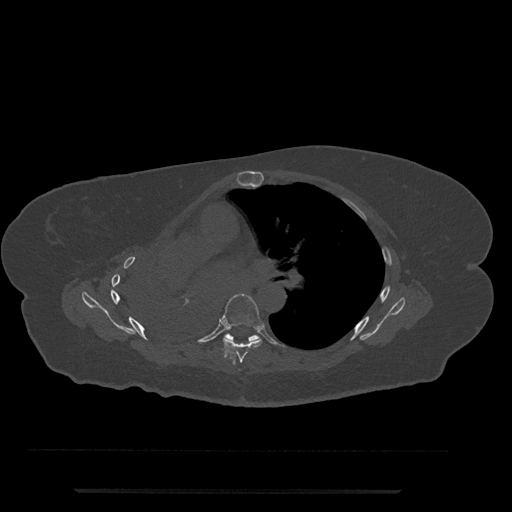
CT including the spine, one axial slice; position 480 of 797 along the scan axis; bone window (W 1800 / L 400 HU); 0.5 mm slice thickness; 512 × 512 image matrix, field of view 440 × 440 mm. Patient: female, 51 years. From the clinical record (not read from this slice): primary cancer: neuro; vertebrae with lytic lesions (as recorded): T8.
Outlined on this slice (semi-automatically segmented with operator editing):
- T6 vertebra: bounding box [x1, y1, x2, y2] px = [220, 294, 264, 364]
- T7 vertebra: [225, 333, 260, 341]